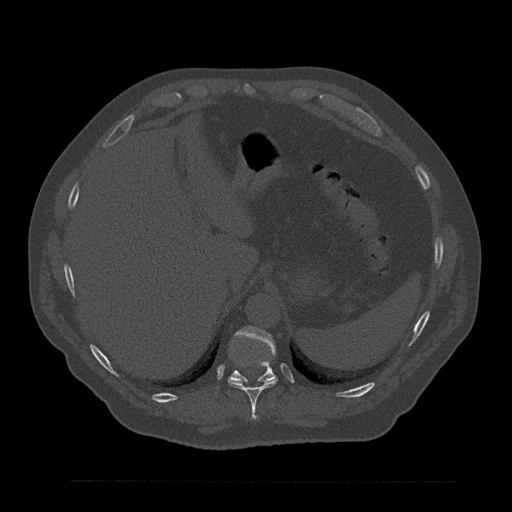
CT including the spine, one axial slice; position 326 of 797 along the scan axis; bone window (W 1800 / L 400 HU); 512 × 512 image matrix, field of view 430 × 430 mm. Patient: male, 61 years. Case-level facts recorded for this patient, not image findings: primary cancer: prostate.
Structures marked on this image (semi-automatically segmented with operator editing):
- T10 vertebra: bounding box [x1, y1, x2, y2] px = [228, 378, 278, 419]
- T11 vertebra: [230, 326, 277, 383]